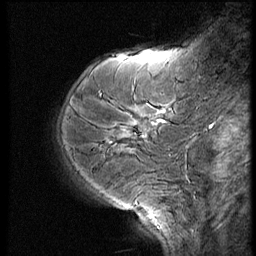
Breast MRI (dynamic contrast-enhanced), one sagittal slice; slice 15 of 52 in the series (ordered by position); dynamic contrast-enhanced series, image 2 of 3 at this slice position (ordered by acquisition); 1.5 T; TE 4.2 ms, TR 9 ms; 2.5 mm slice thickness; 256 × 256 image matrix, field of view 180 × 180 mm. Patient: female, 62 years. Case-level facts recorded for this patient, not image findings: setting: breast cancer imaged before/during neoadjuvant chemotherapy; receptor status: HR-positive, HER2-negative.
Outlined on this slice (semi-automatically segmented with operator editing):
- analysis volume of interest (the breast-tissue region the enhancement analysis was run in; not a lesion): box from (x=67, y=94) to (x=182, y=177) px
- tumour enhancement mask (voxels above the 140 % enhancement threshold inside the analysis volume of interest): (x=144, y=111)–(x=167, y=138)